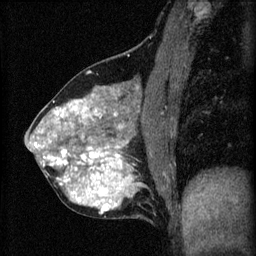
Breast MRI (dynamic contrast-enhanced), one sagittal slice; slice 27 of 60 in the series (ordered by position); 3 images stored at this slice position (order not interpretable as contrast timing); 1.5 T; TE 4.2 ms, TR 8.2 ms; 2 mm slice thickness; 256 × 256 image matrix. Patient: female, 40 years.
Annotated regions visible in this slice (semi-automatically segmented with operator editing):
- analysis volume of interest (the breast-tissue region the enhancement analysis was run in; not a lesion): bounding box [x1, y1, x2, y2] px = [26, 76, 175, 219]
- tumour enhancement mask (voxels above the 70 % enhancement threshold inside the analysis volume of interest): [34, 94, 141, 215]